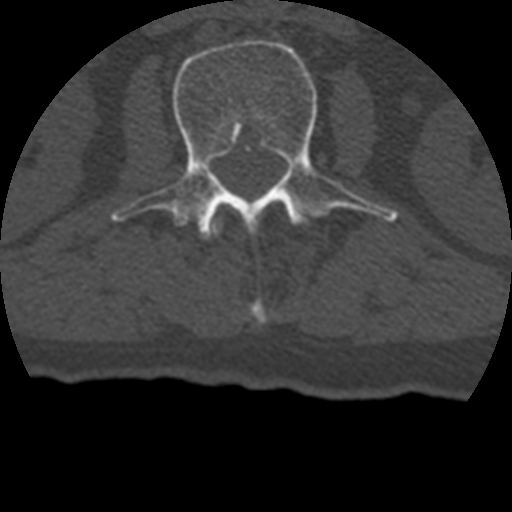
CT including the spine, one axial slice. Bone window (W 1800 / L 400 HU). 512 × 512 image matrix. Patient age 69 years. From the clinical record (not read from this slice): primary cancer: prostate.
Structures marked on this image (semi-automatically segmented with operator editing):
- L1 vertebra: bounding box (x1, y1, x2, y2) in pixels: (210, 217, 267, 324)
- L2 vertebra: (113, 39, 397, 245)